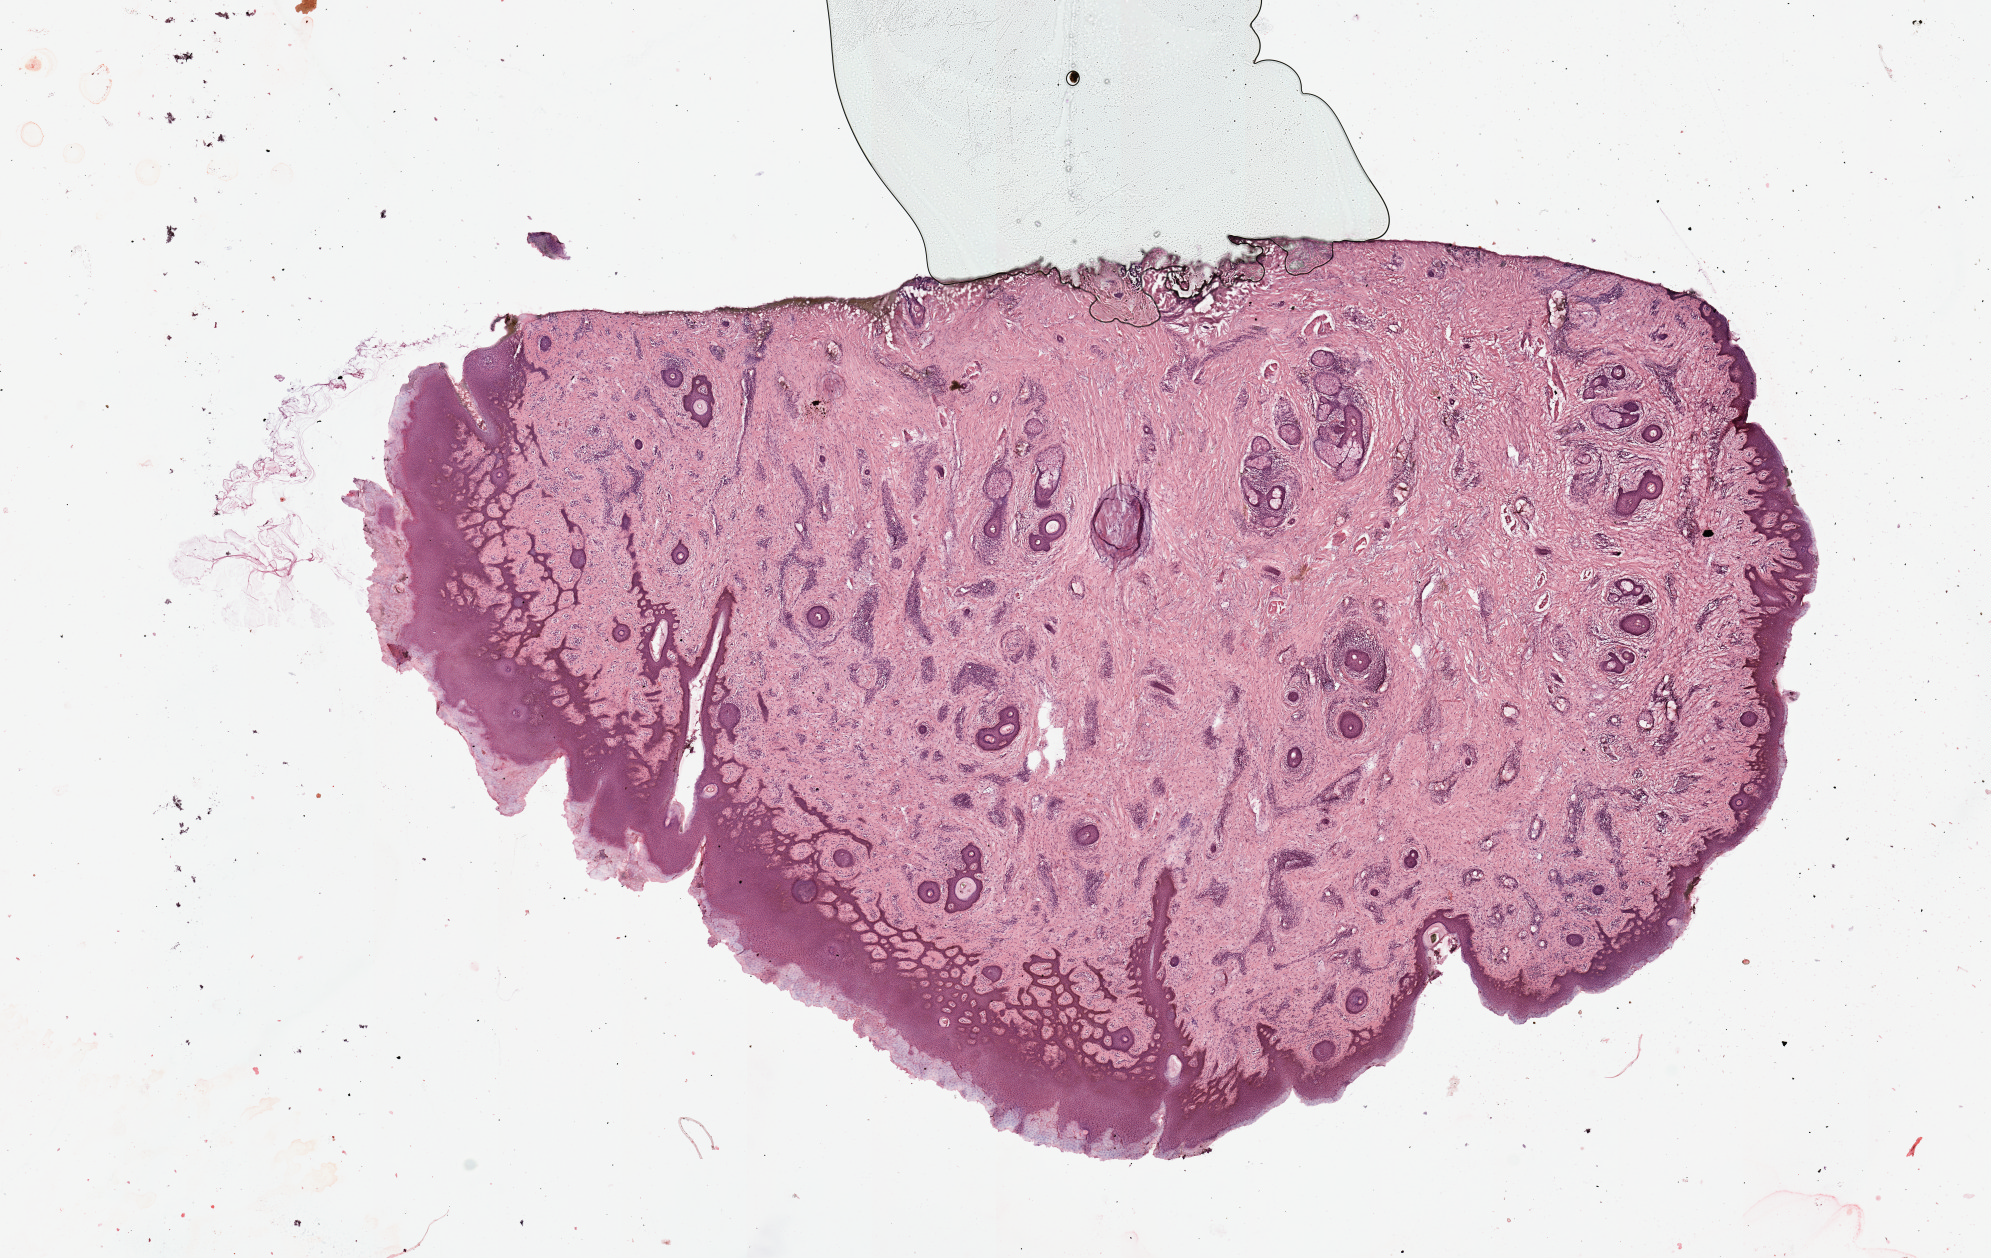
Hematoxylin and eosin (H&E) stained whole-slide image — whole scanned area (about 15.8 x 10.0 mm) shown as a low-resolution overview, normal (non-tumour) tissue (melanoma cohort); sampled site not recorded. 54-year-old male patient.
This section: normal (non-tumour) tissue from the same patient. Patient diagnosis (cohort enrolment): cutaneous melanoma (skin).